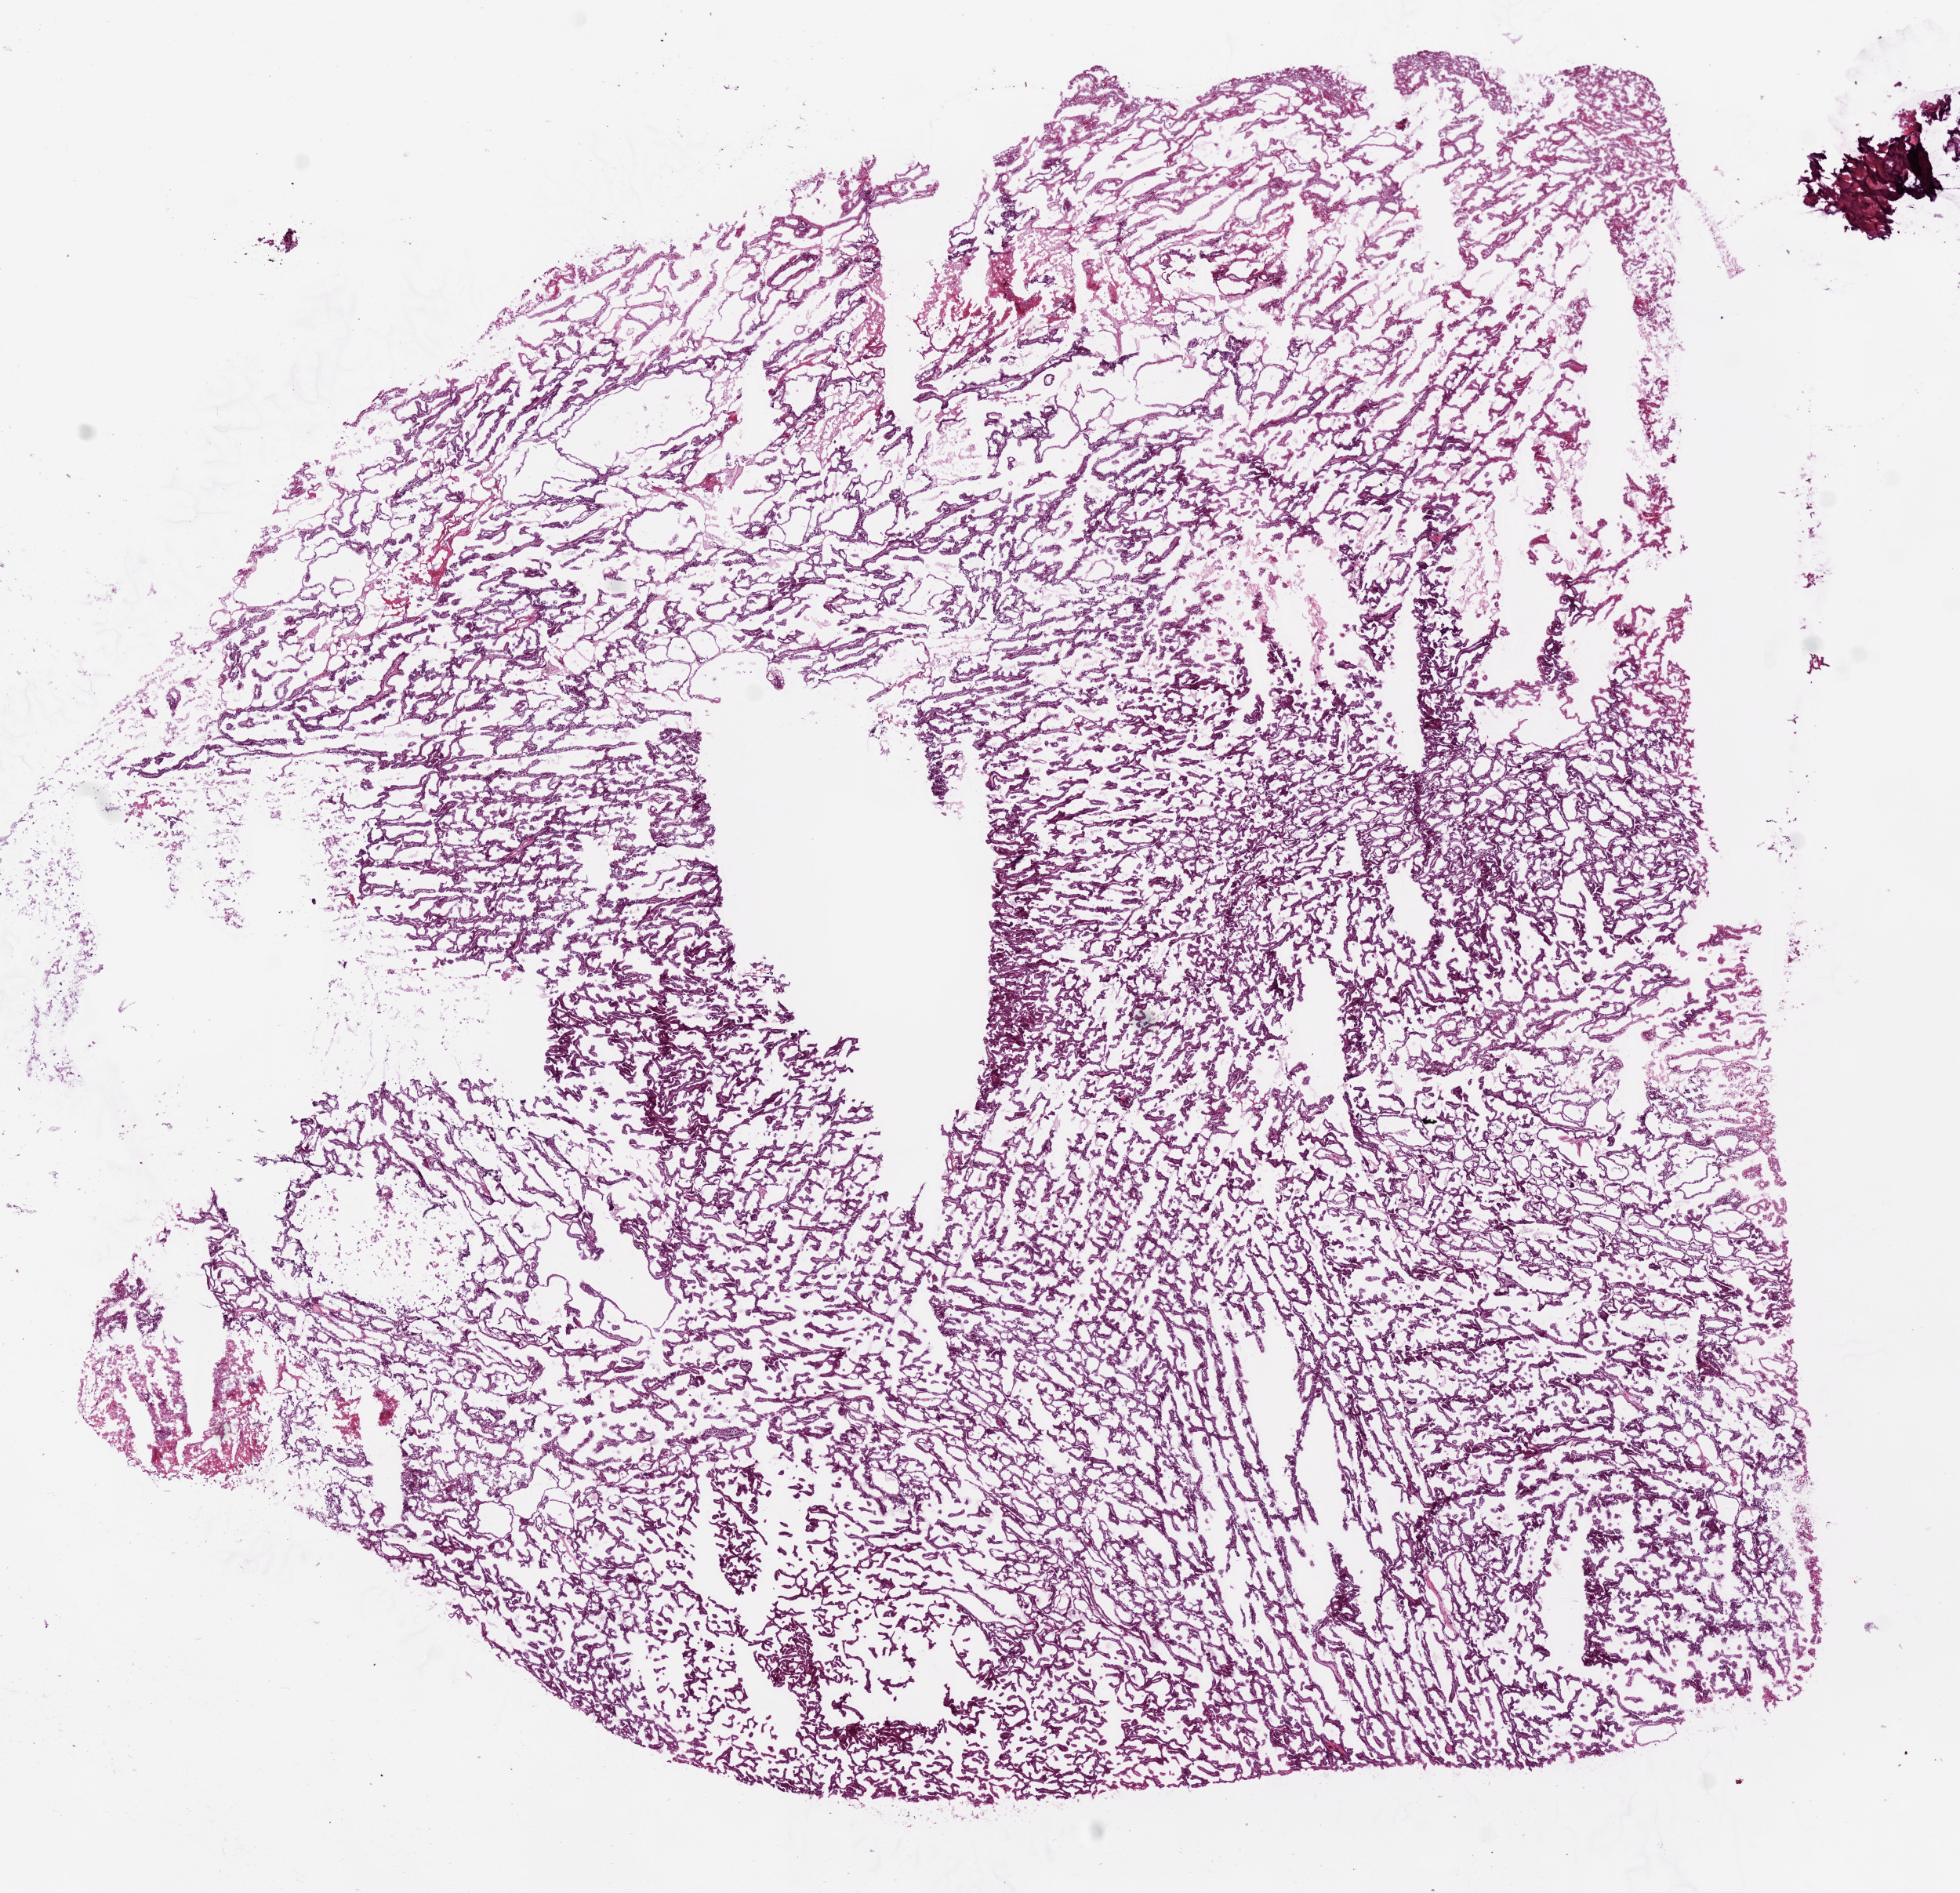
Whole-slide histology image, H&E-stained — a low-resolution overview of the entire scanned area, about 10.0 x 9.7 mm (from a 20x scan), frozen section, primary tumour sample from the kidney. Male, age 74 years at initial diagnosis.
Pathologic diagnosis: Papillary adenocarcinoma, NOS.